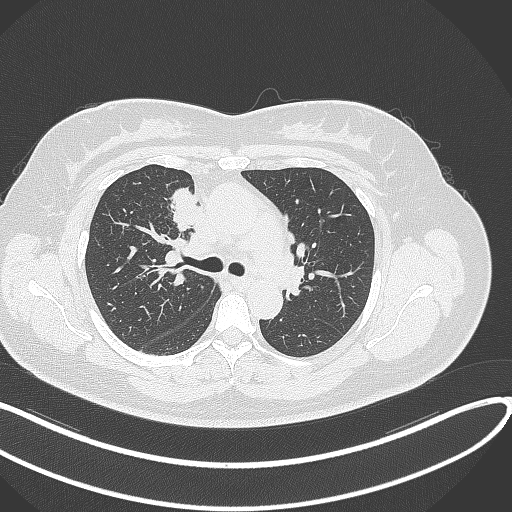
Chest CT, one axial slice; 120 kVp; lung window (W 1500 / L -600 HU); 1 mm slice thickness; 512 × 512 image matrix, field of view 400 × 400 mm. Female patient, age 46 years. From the clinical record (not read from this slice): clinical TNM (as recorded): T2a N1 M0.
Structures marked on this image (bounding box drawn by a radiologist):
- lung tumour (recorded histology: adenocarcinoma): bounding box (x1, y1, x2, y2) in pixels: (169, 184, 201, 232)